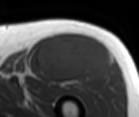
MRI of an extremity soft-tissue mass, one axial slice; slice 64 of 86 in the series (ordered by position); MR volume resampled by the dataset authors to the PET/CT grid (not the native acquisition matrix); 3.27 mm slice thickness; 139 × 117 image matrix, field of view 136 × 114 mm. Male patient. Case-level facts recorded for this patient, not image findings: histological type: extraskeletal osteosarcoma; grade: high; site of the primary tumour: thigh.
Outlined on this slice (expert contour drawn on MRI and transferred to this co-registered scan by the dataset authors):
- gross tumour volume (mass): bounding box <38,34,112,83> (left, top, right, bottom; pixels)